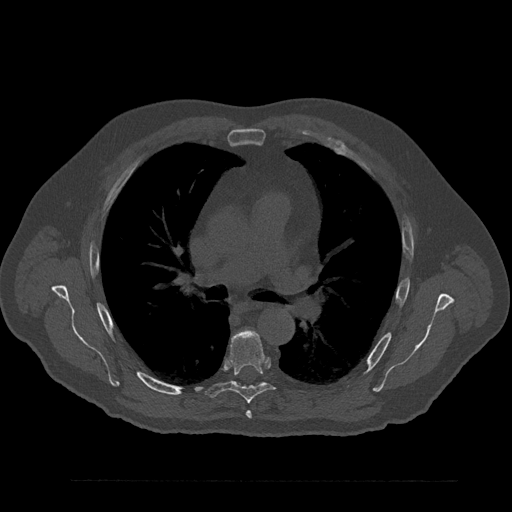
CT including the spine, one axial slice; position 559 of 797 along the scan axis; reconstruction kernel Br40s/3; 120 kVp; bone window (W 1800 / L 400 HU); 0.5 mm slice thickness; 512 × 512 image matrix, field of view 430 × 430 mm. Male patient, age 61 years. Case-level facts recorded for this patient, not image findings: primary cancer: prostate.
Structures marked on this image (semi-automatically segmented with operator editing):
- T5 vertebra: bounding box [x1, y1, x2, y2] px = [246, 411, 252, 419]
- T6 vertebra: [205, 330, 275, 403]